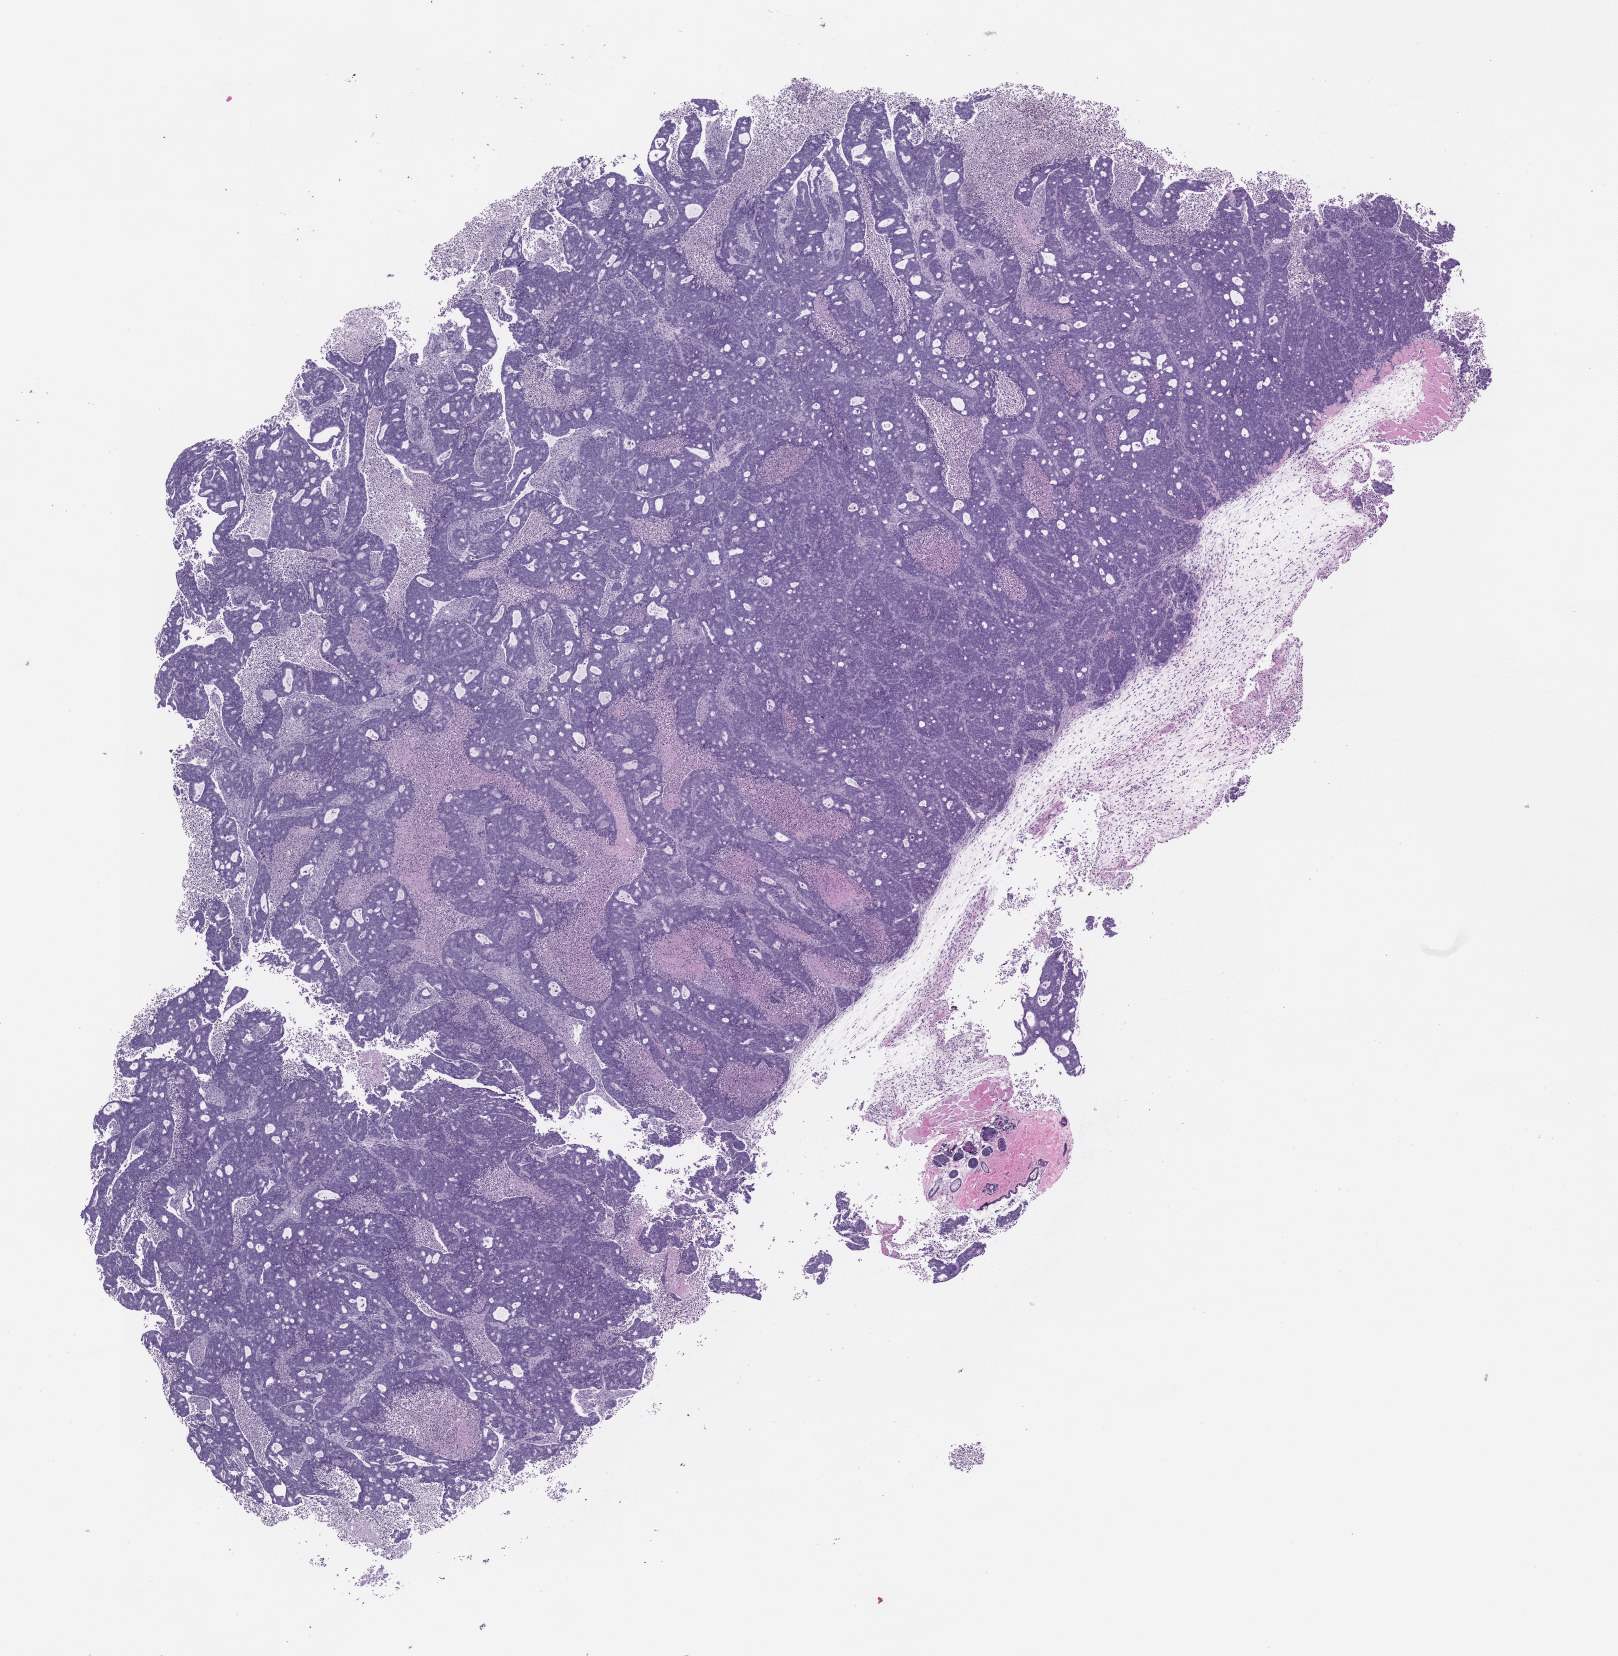
Whole-slide image, H&E: patient-derived xenograft (human tumor grown in a mouse), passage 0 — low-resolution overview of the scanned area, about 13.0 x 13.3 mm; formalin-fixed, paraffin-embedded (FFPE) tissue; originating tumor site category: colon.
* originating patient diagnosis: Colon Adenocarcinoma